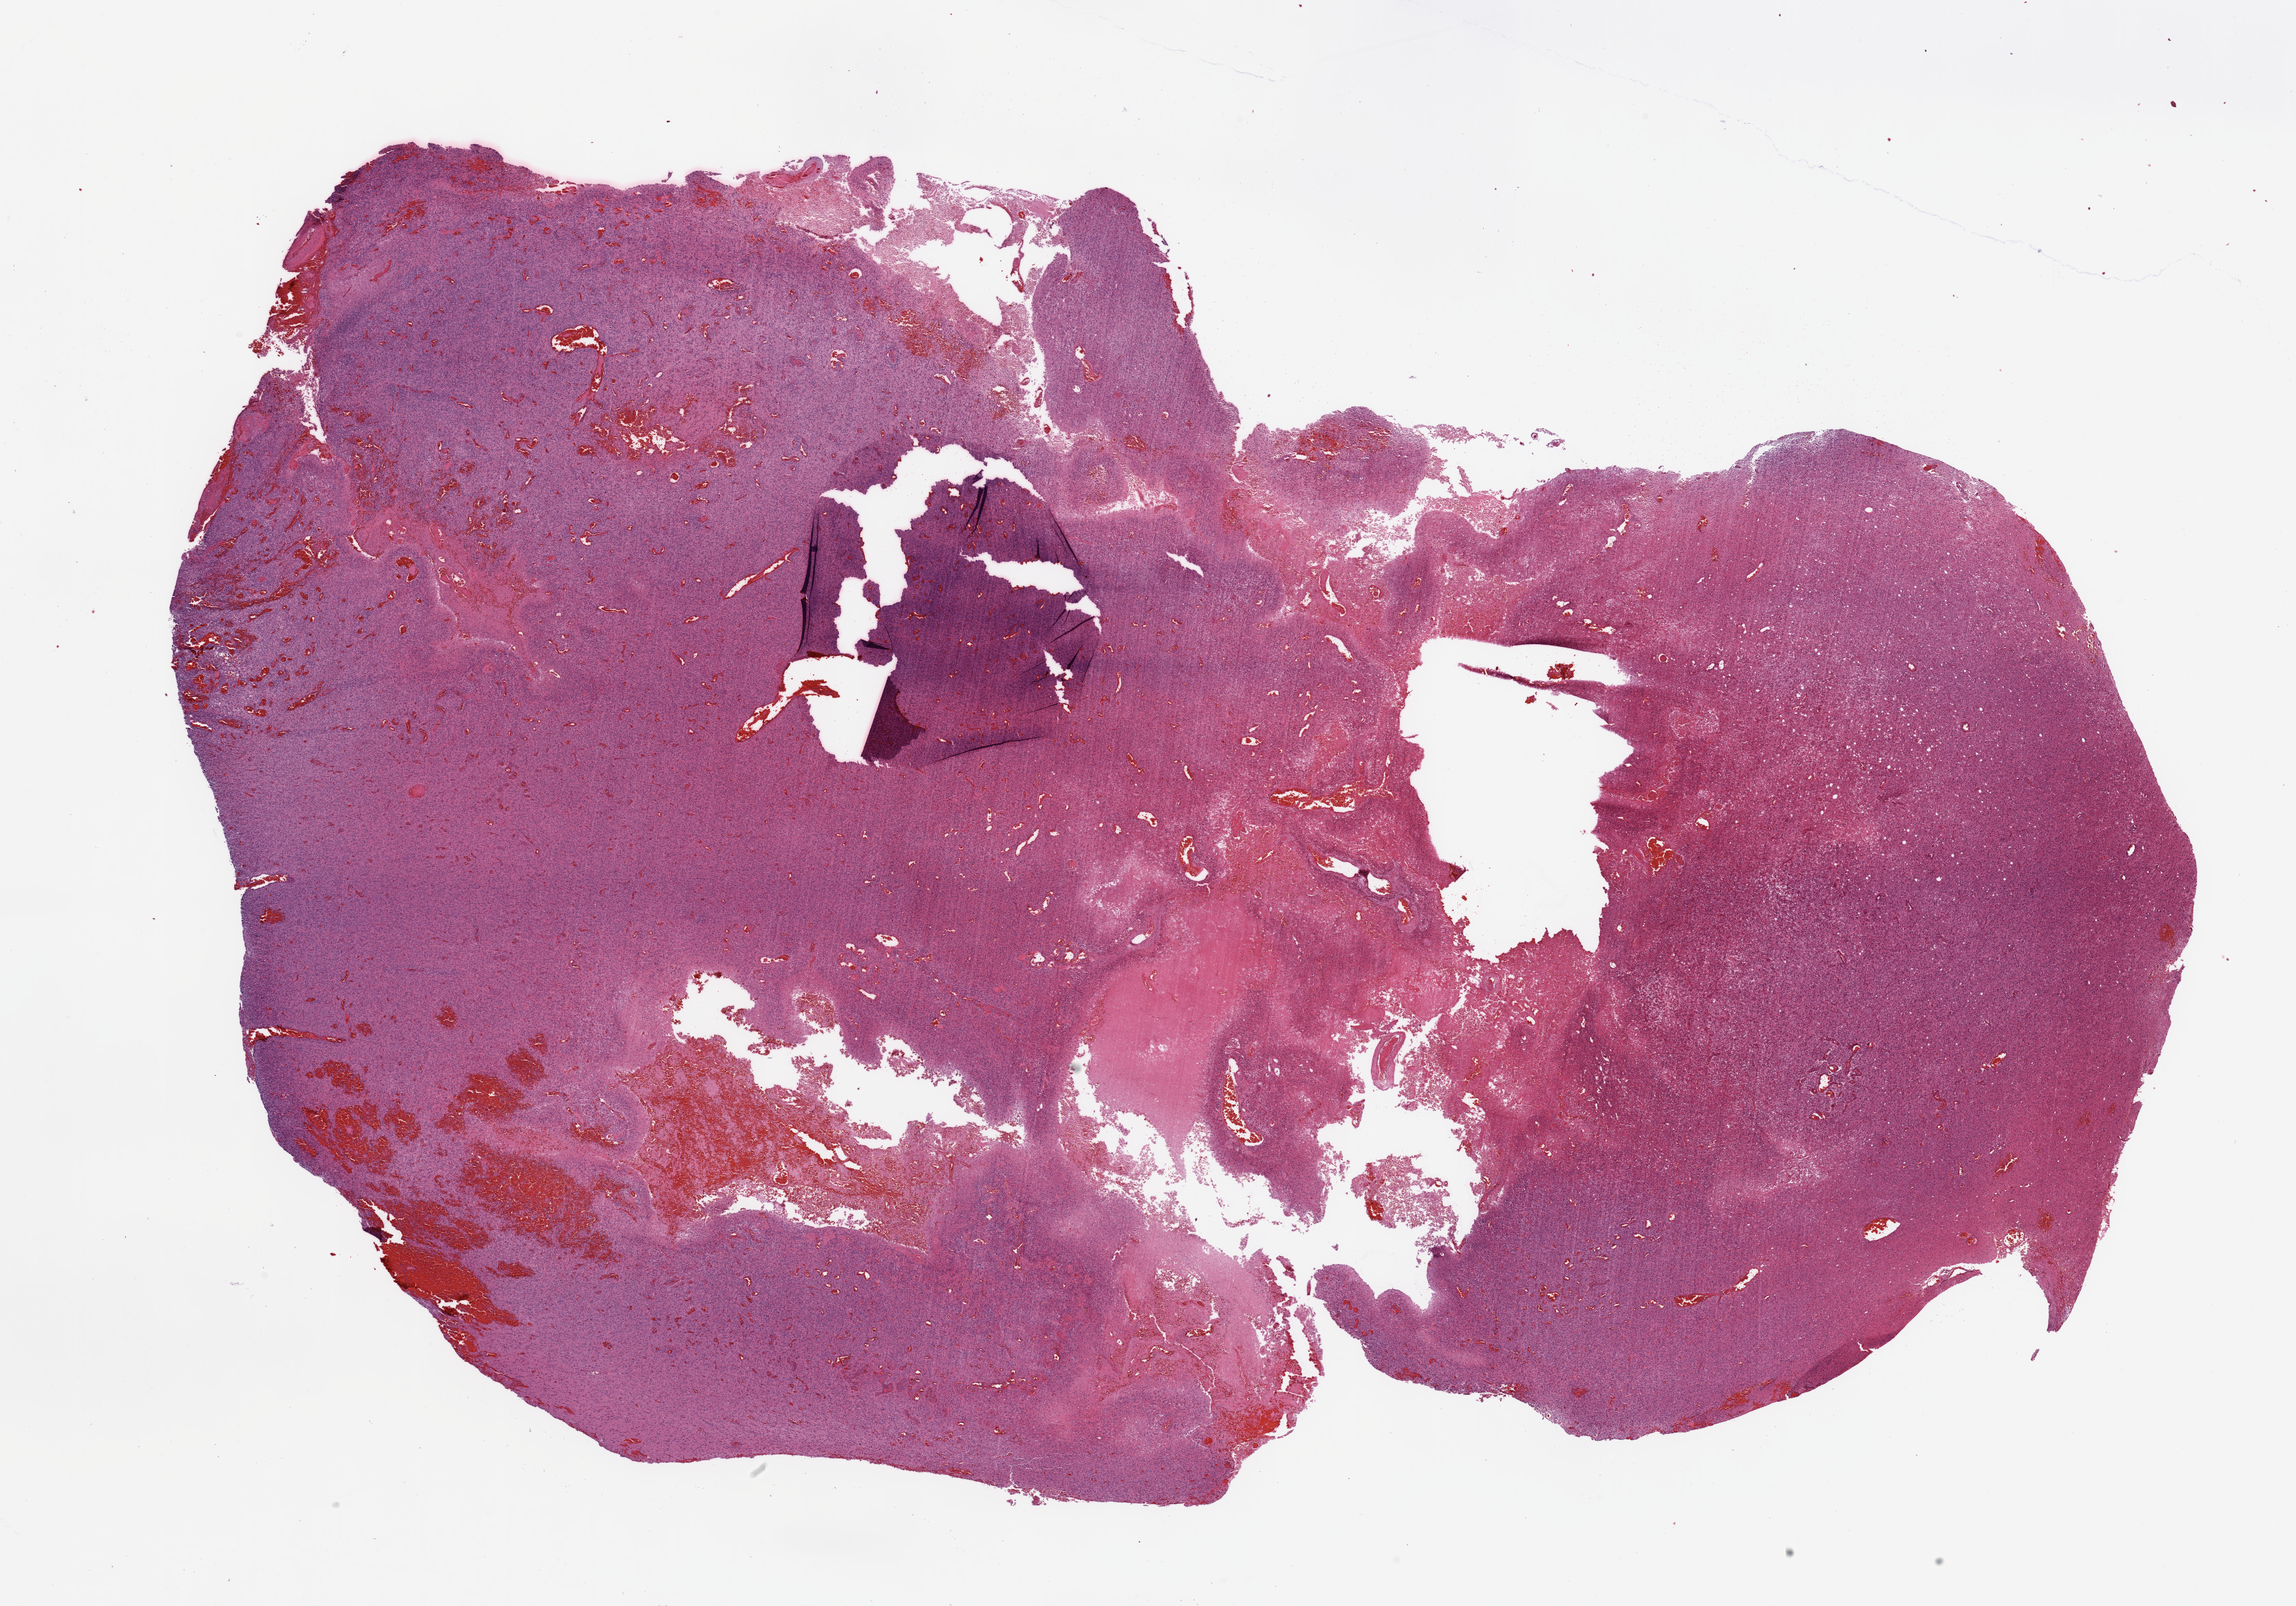
H&E whole-slide image, shown as a low-resolution overview of the whole scanned area (about 26.6 x 18.6 mm); brain, tumour tissue. Female, 64 y/o.
Primary tumour site (as recorded): frontal lobe. Diagnosis: Glioblastoma.